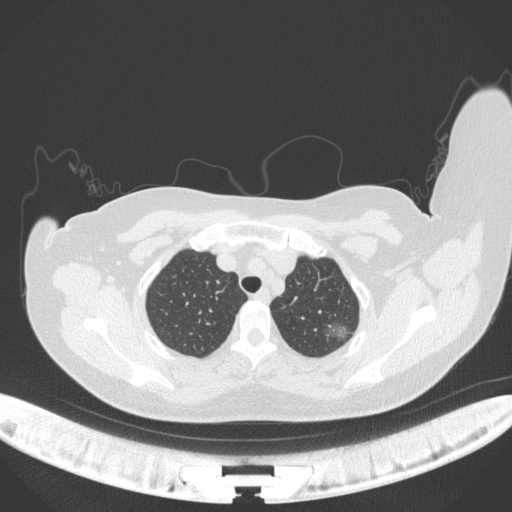
Chest CT, one axial slice; slice 309 of 386 in the series (ordered by position); reconstruction kernel B31f; 120 kVp; lung window (W 1500 / L -600 HU); 1 mm slice thickness; 512 × 512 image matrix, field of view 400 × 400 mm. Patient: female, 58 years. Case-level facts recorded for this patient, not image findings: clinical TNM (as recorded): T1c N0 M0.
Outlined on this slice (bounding box drawn by a radiologist):
- lung tumour (recorded histology: adenocarcinoma): bounding box <324,318,351,341> (left, top, right, bottom; pixels)